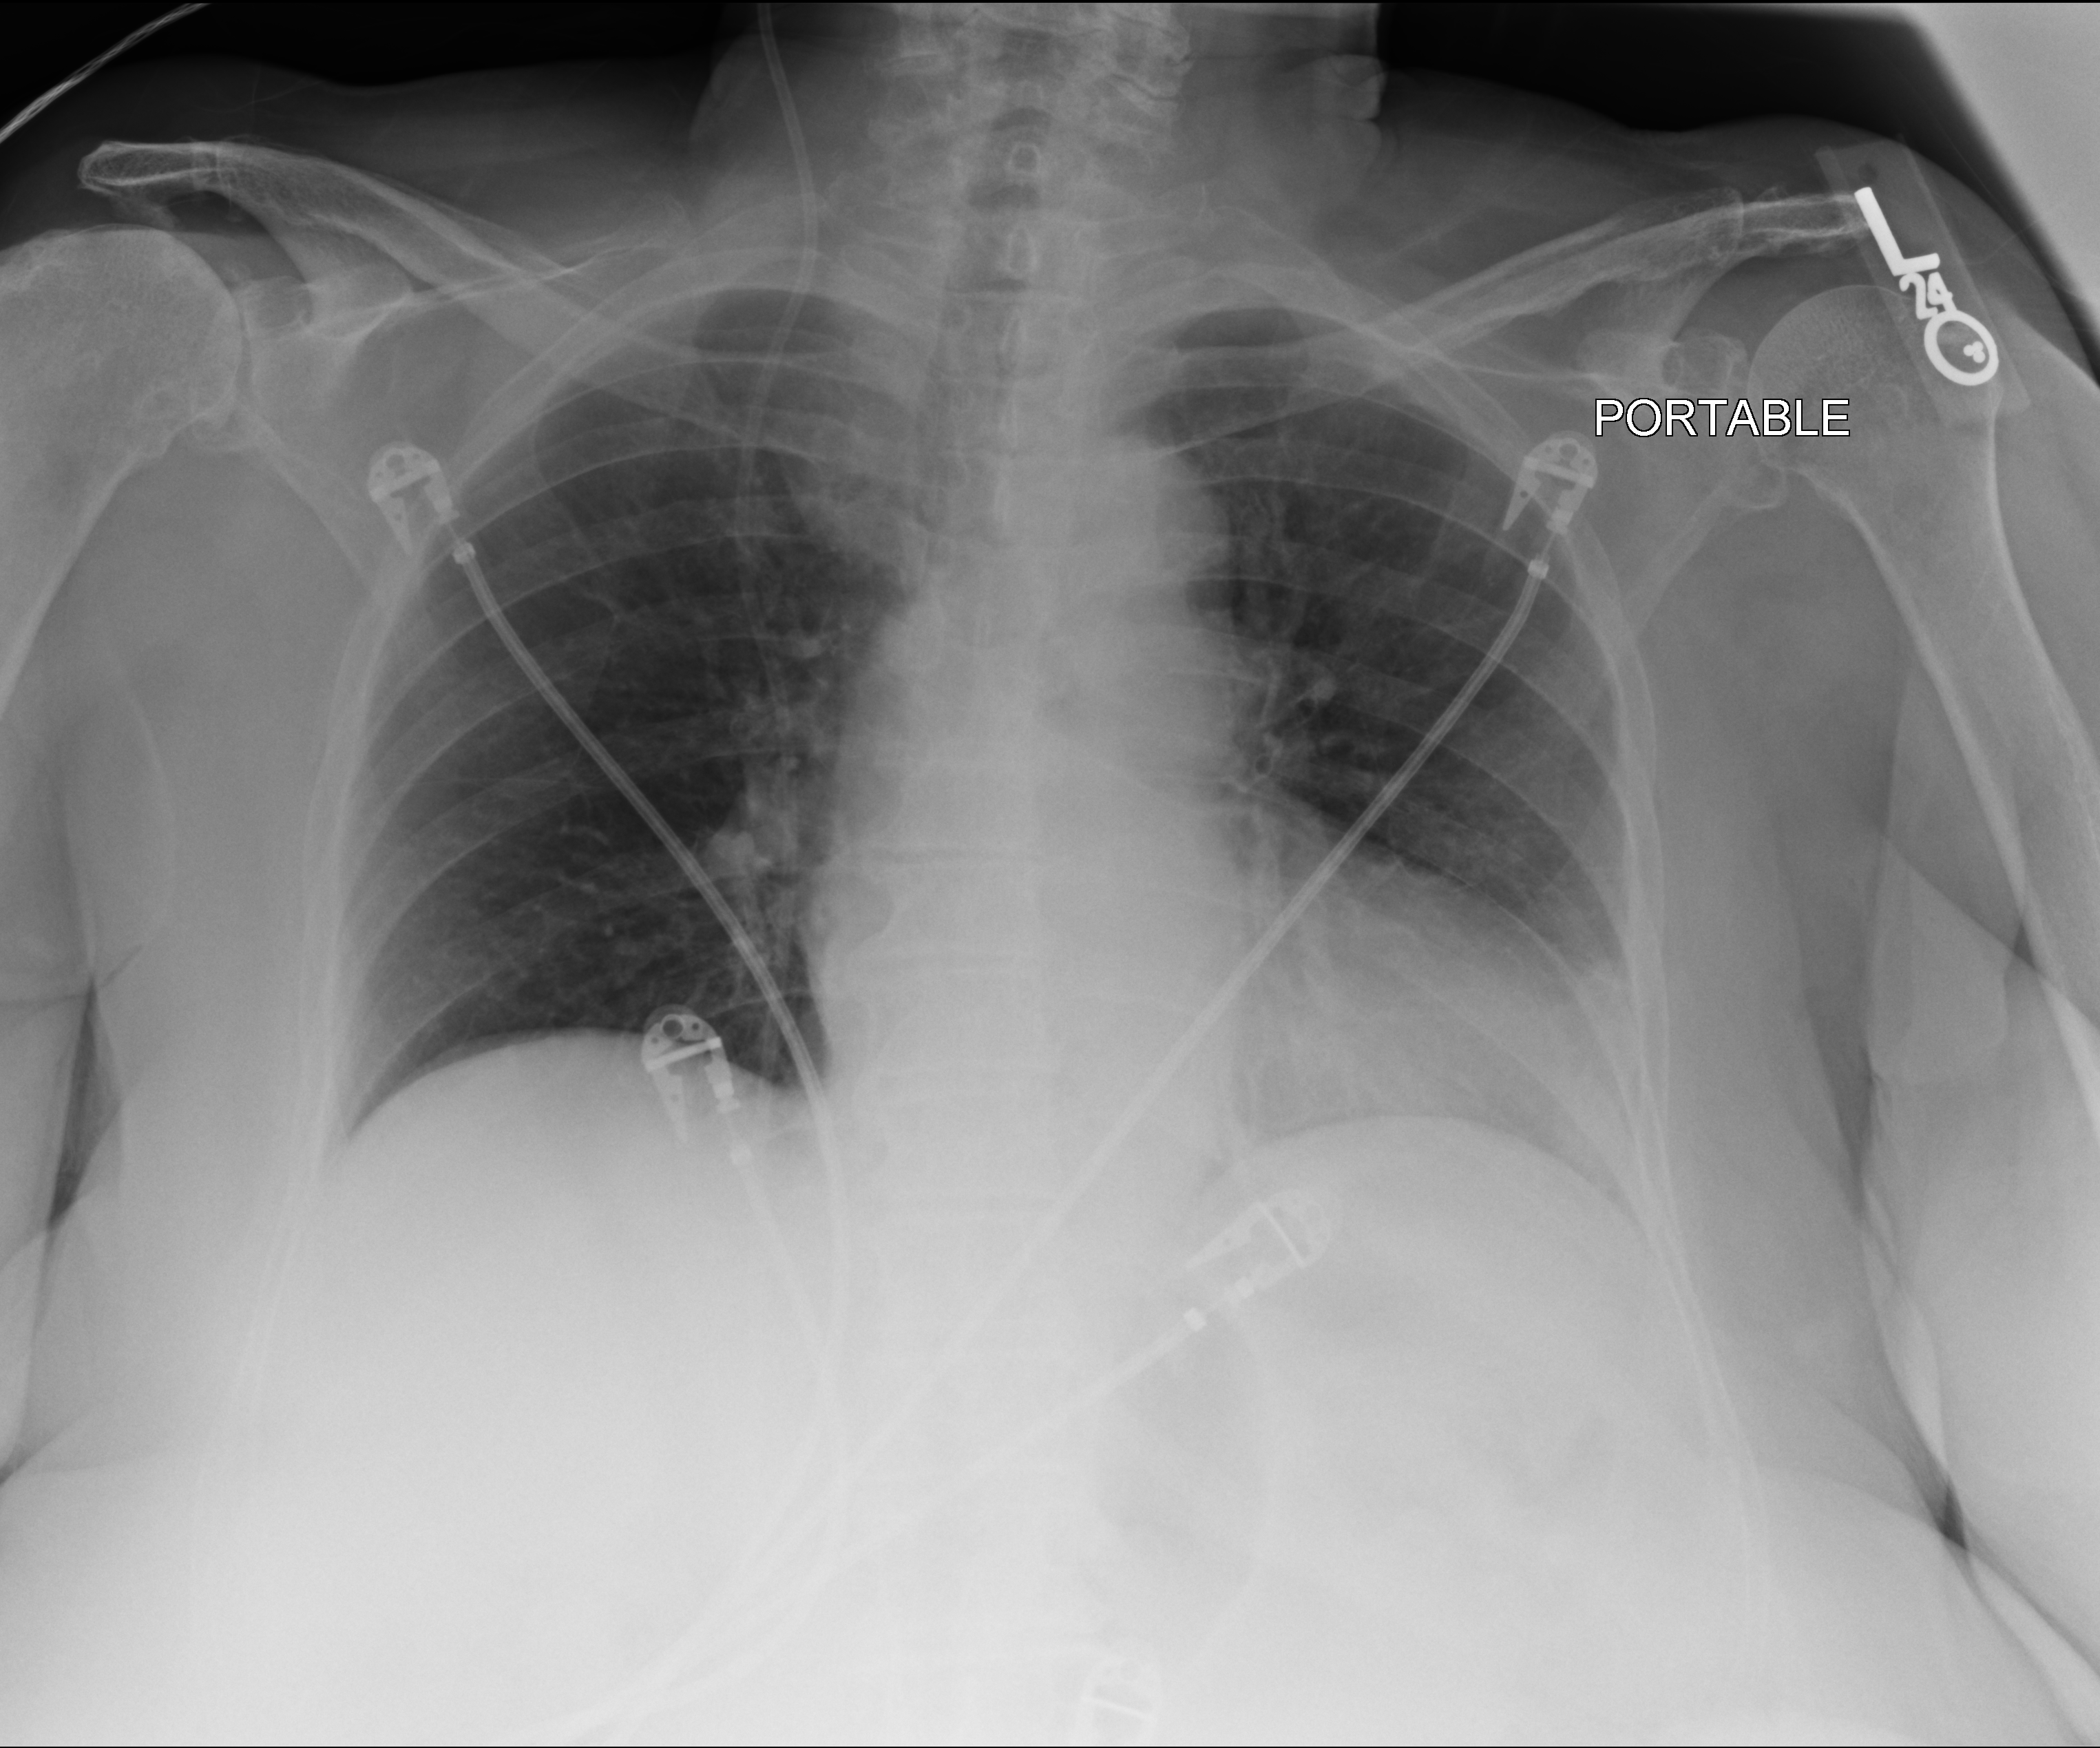
Portable chest radiograph, anteroposterior (AP) projection. Female patient hospitalised with COVID-19, age 75–90 years.
Admission-level facts for this patient (not findings on this image; timing relative to this image not recorded): admitted to intensive care during this hospital stay: yes; other chronic lung disease (admission record): no; length of hospital stay: 29 days.